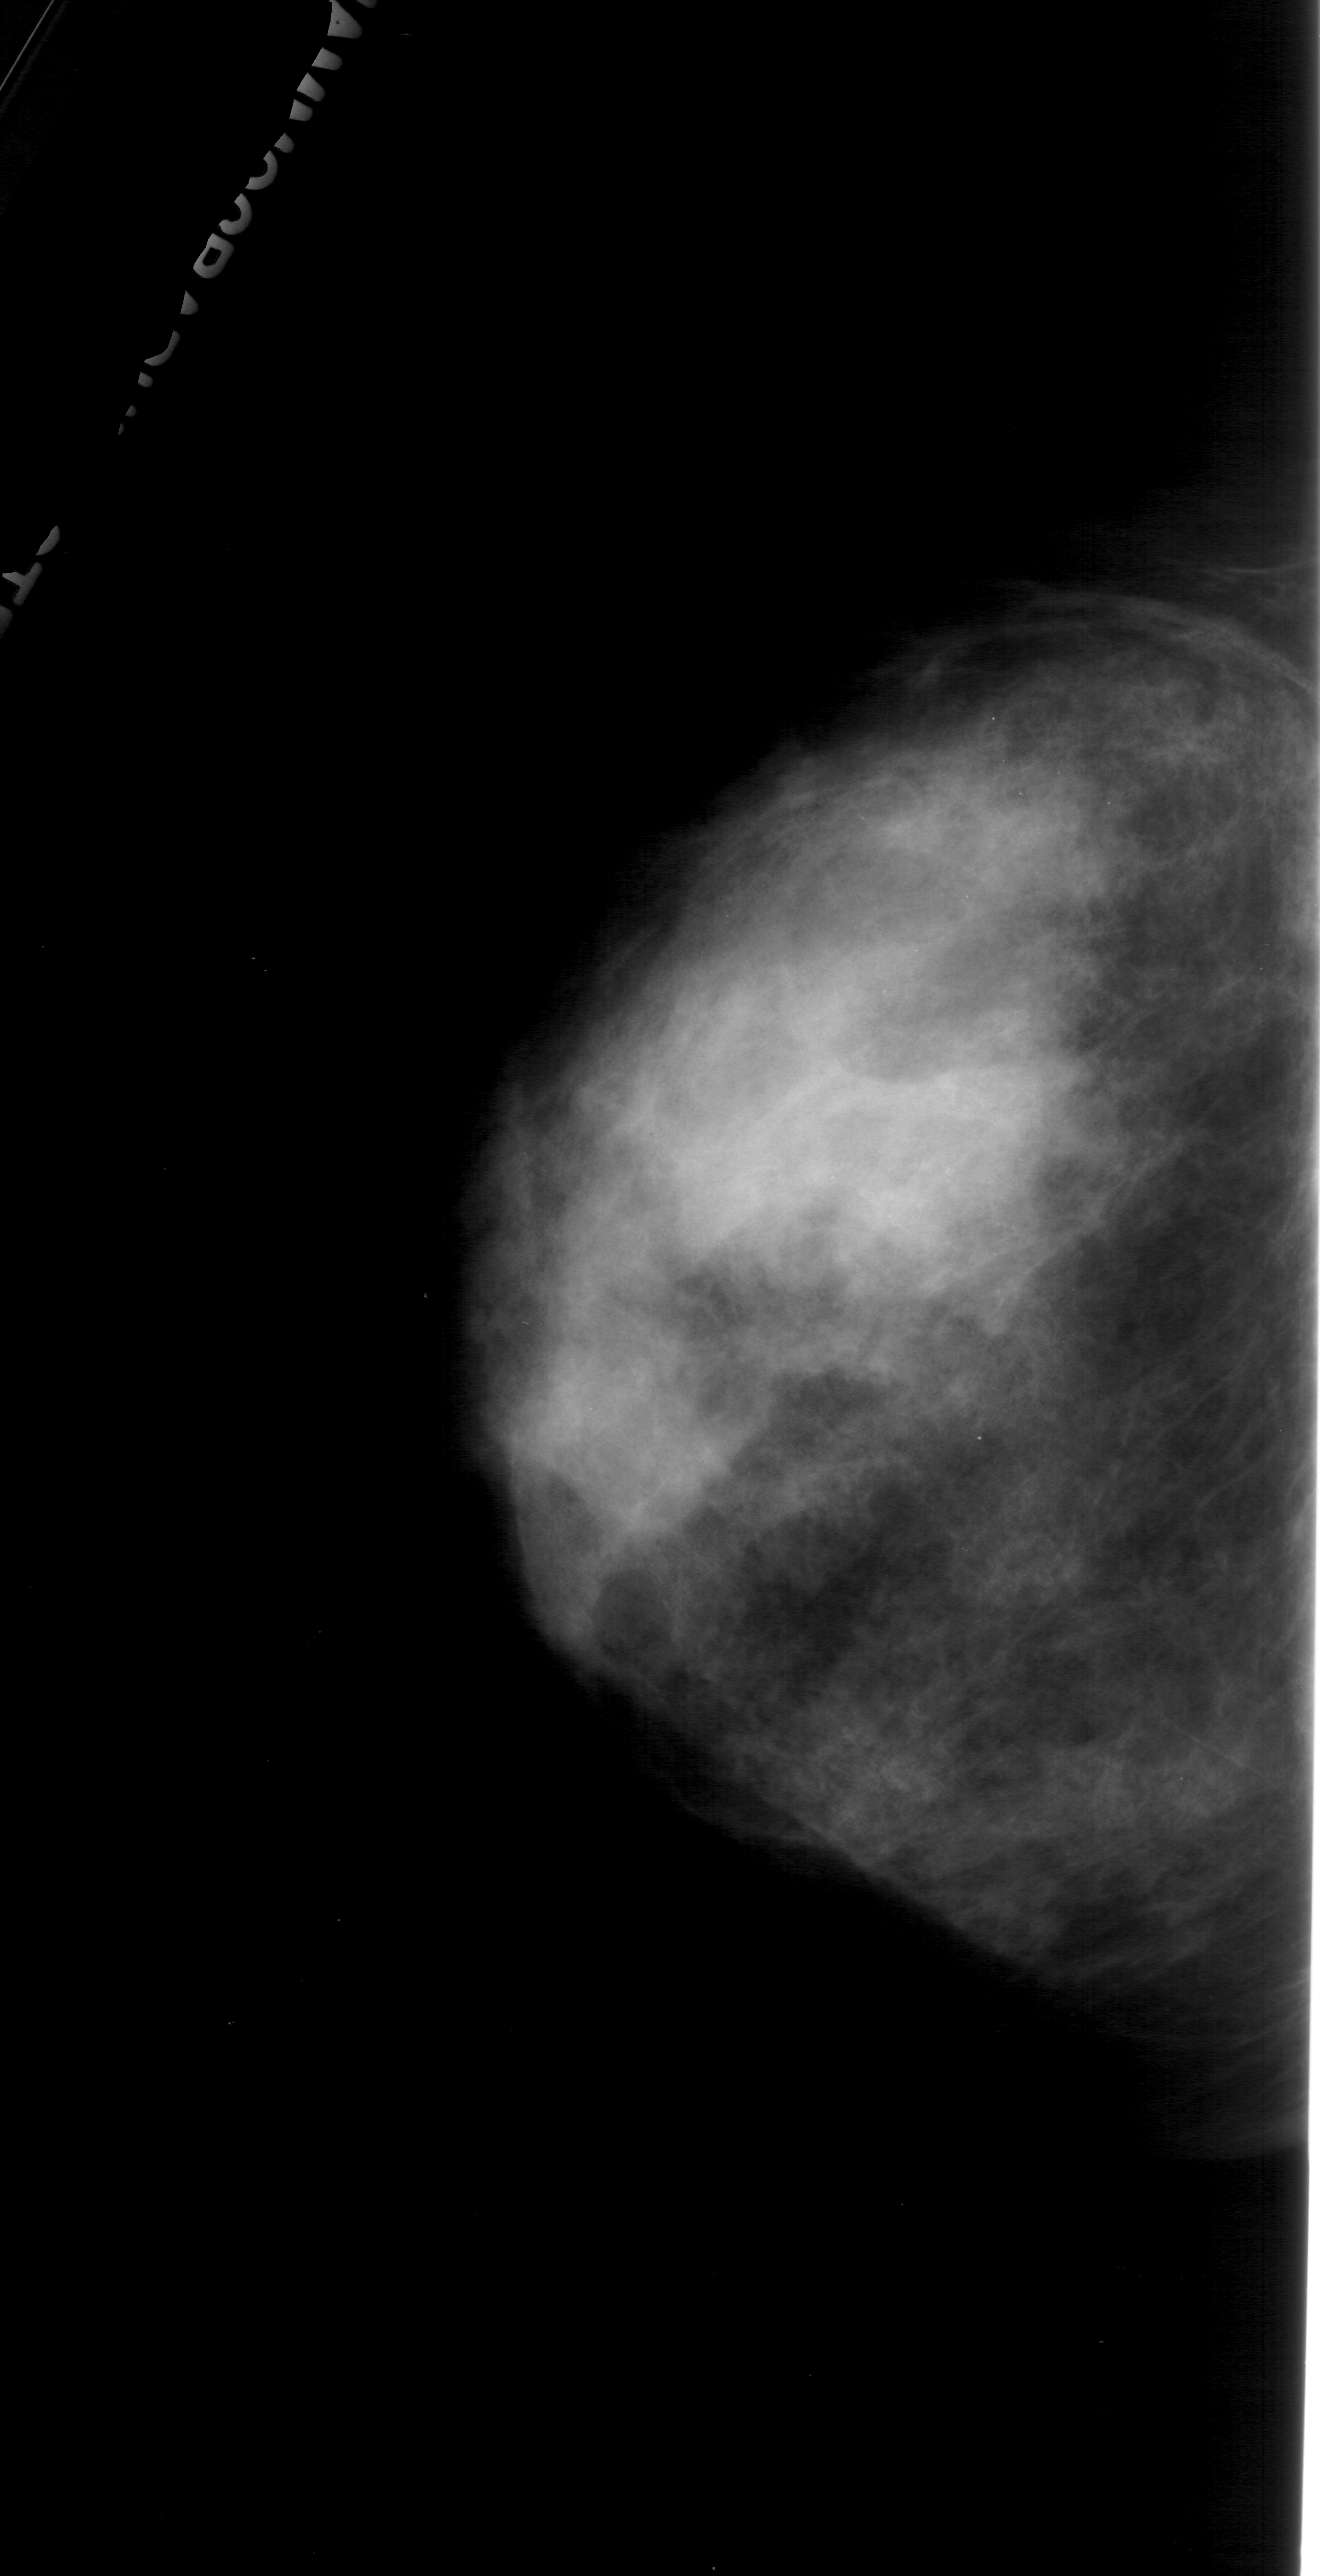
Mammogram (digitized film). Left breast. Craniocaudal (CC) view. BI-RADS breast density category 4 (scale 1–4). 1320 × 2576 image matrix.
Expert-marked regions of interest on this film, with their recorded descriptors:
- calcifications, morphology pleomorphic, distribution segmental; BI-RADS assessment category 4; subtlety rating 1 on a 1 (subtle) to 5 (obvious) scale; pathology (as recorded): malignant: bounding box [x1, y1, x2, y2] px = [551, 744, 1087, 1339]